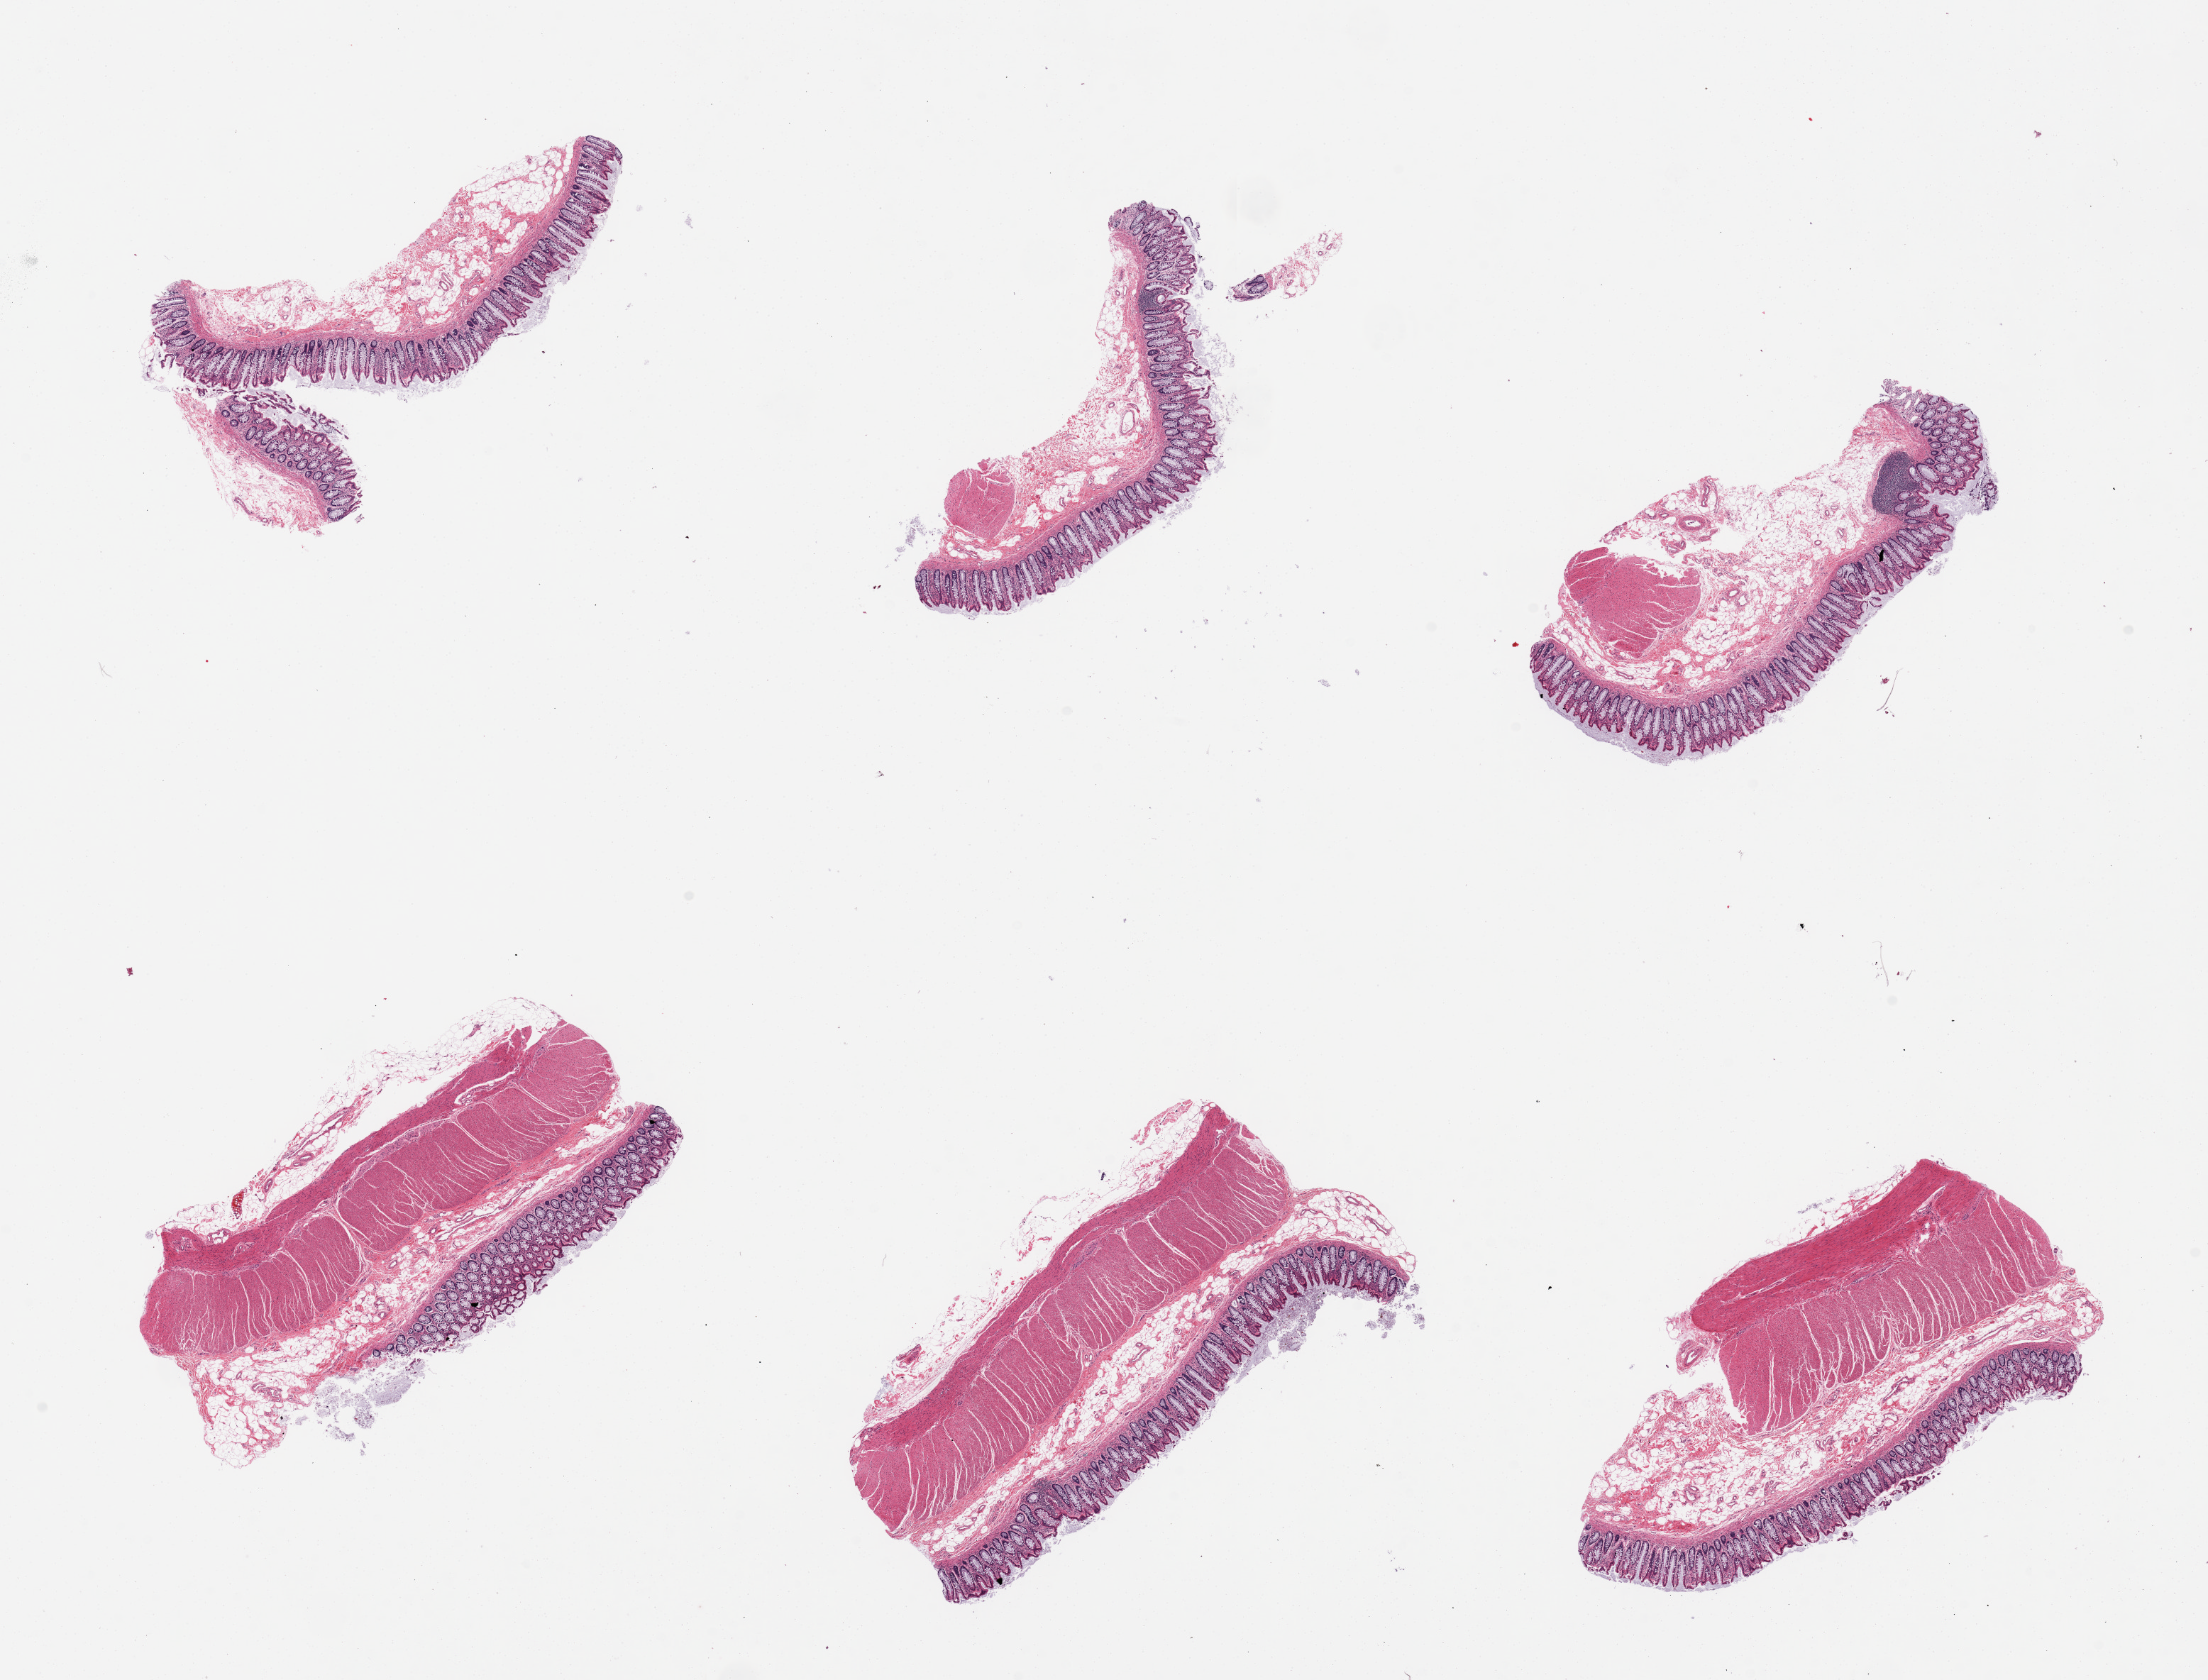
Hematoxylin and eosin (H&E) whole-slide image, low-resolution overview of the scanned area, about 24.6 x 18.7 mm (slide scanned at 20x); PAXgene-fixed, paraffin-embedded tissue; target tissue: ileum; donor tissue sample. Donor: female.
Pathologist's review note for this sample: 6 pieces, colon, not ileum.